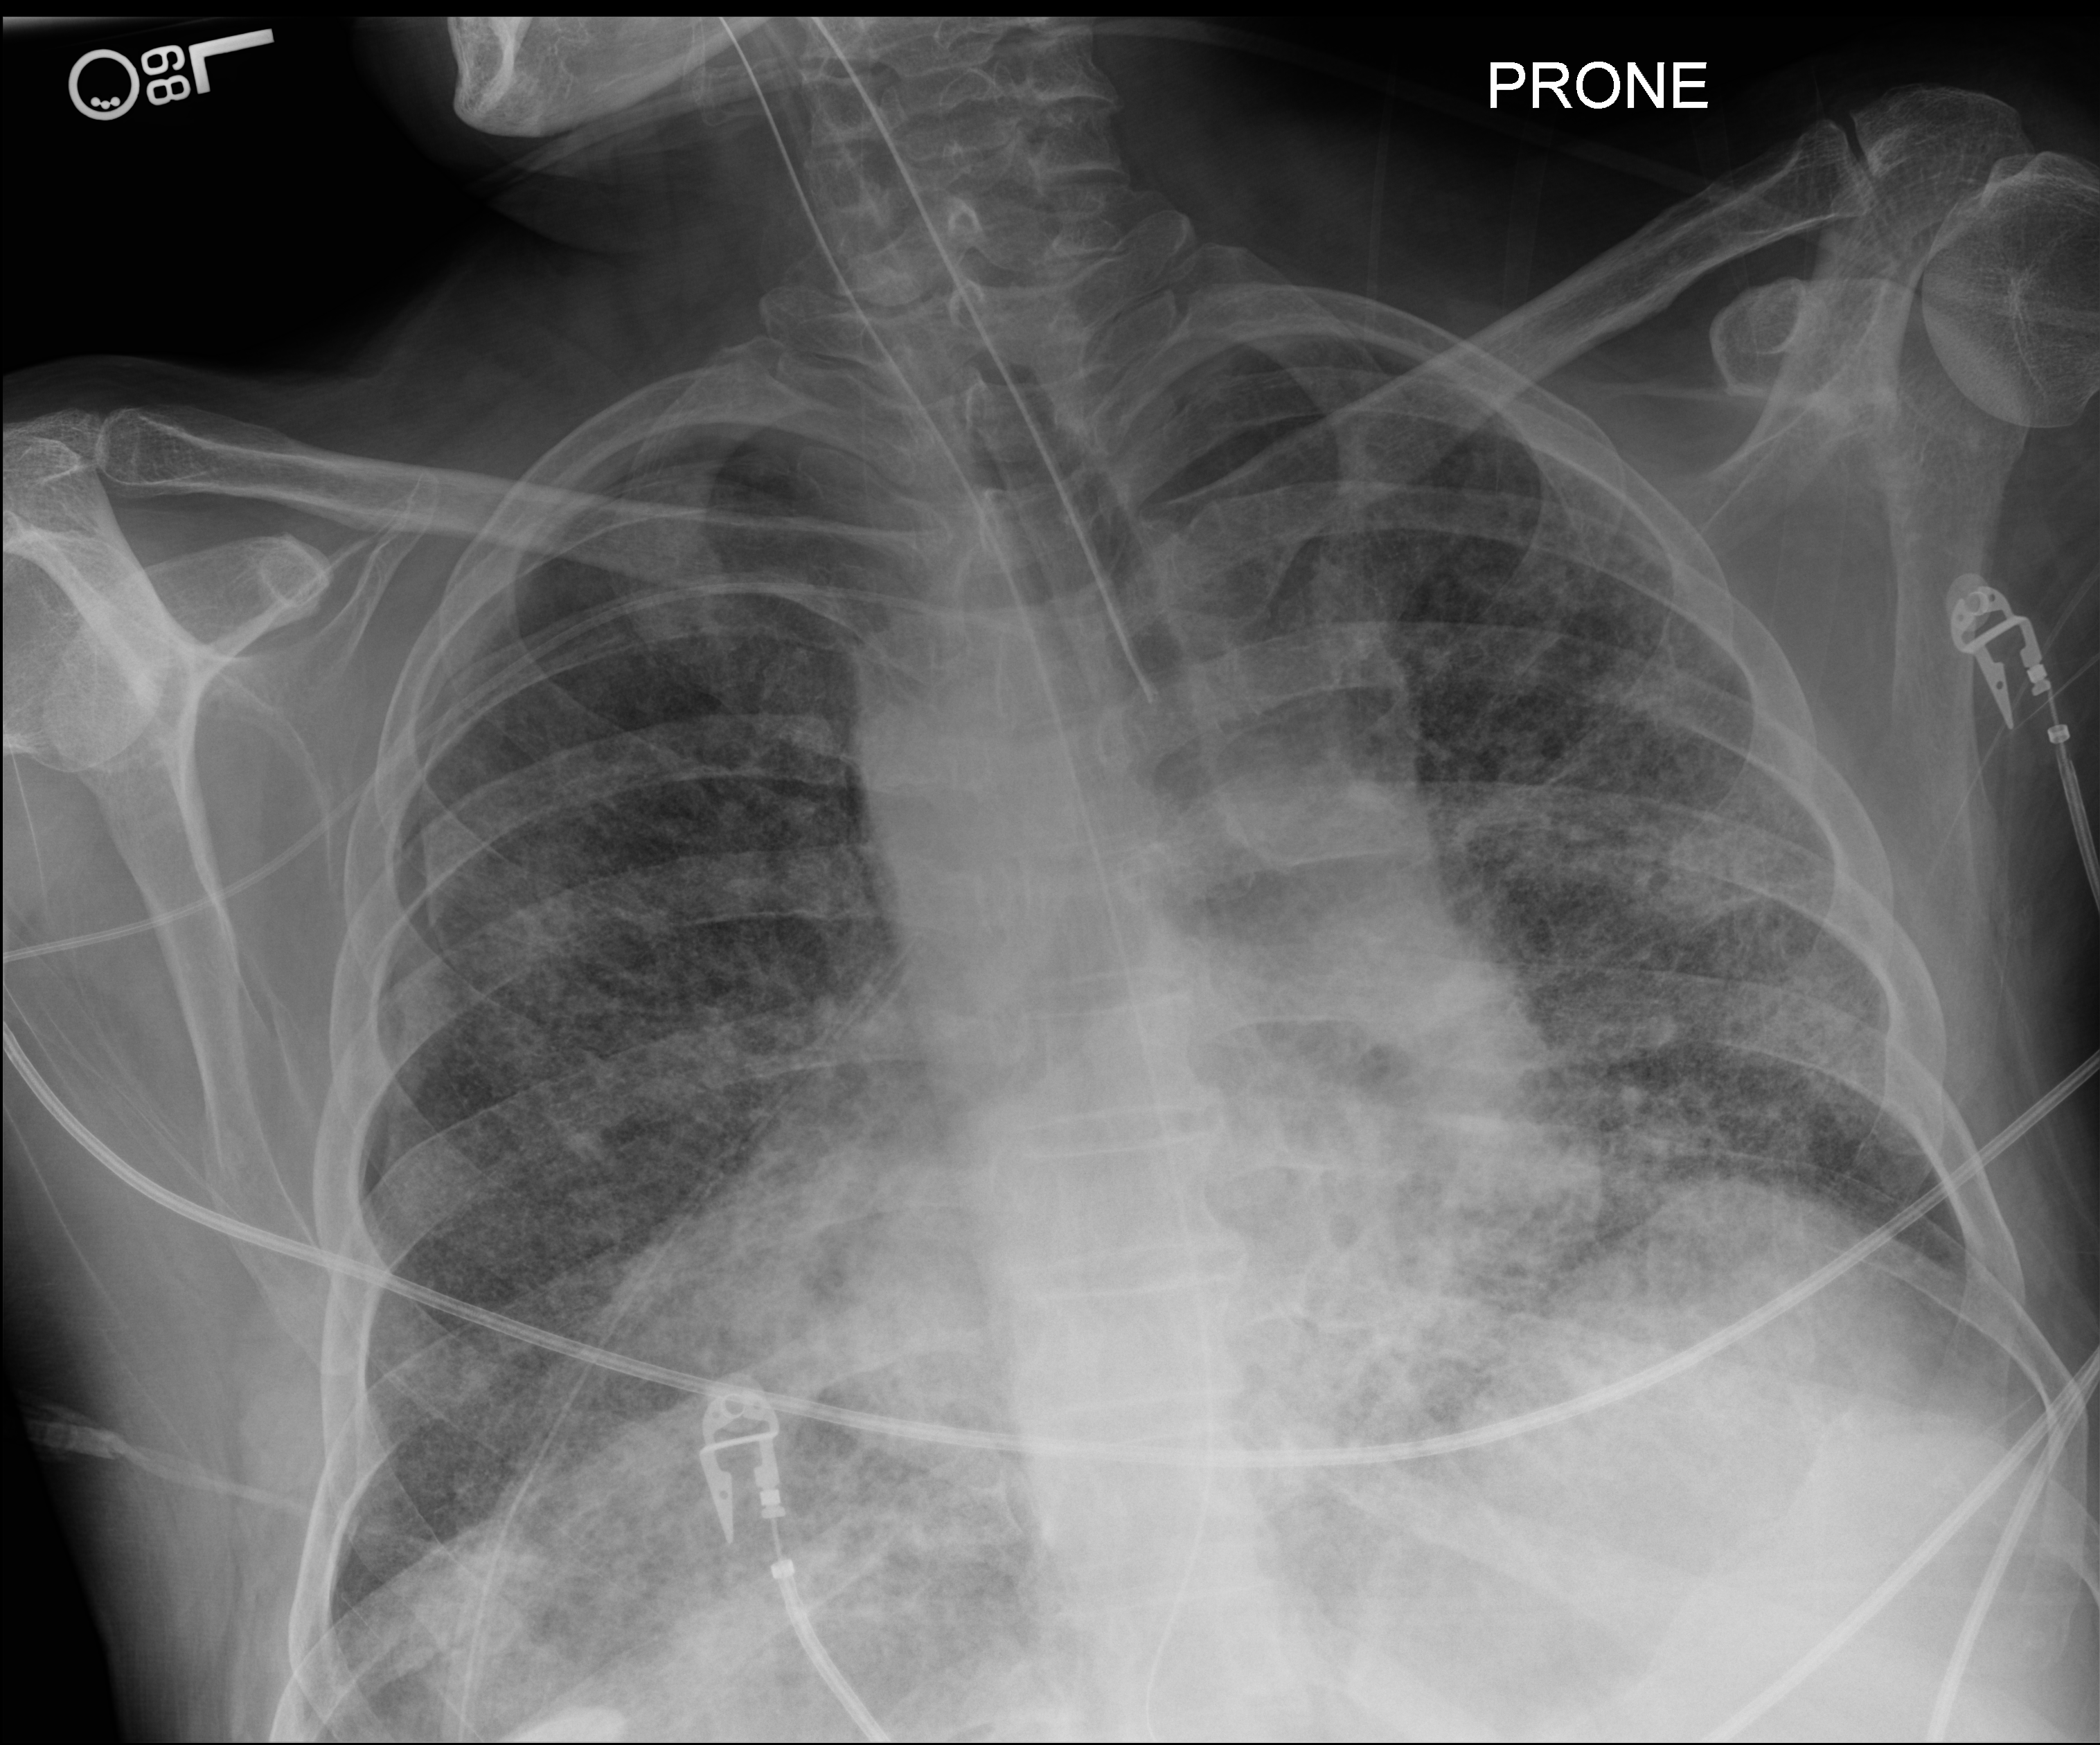
Chest X-ray; posteroanterior (PA) projection. Patient hospitalised with COVID-19; male, aged 60–74 years.
Admission-level facts for this patient (not findings on this image; timing relative to this image not recorded): length of hospital stay: 54 days; mechanically ventilated during this hospital stay: yes.